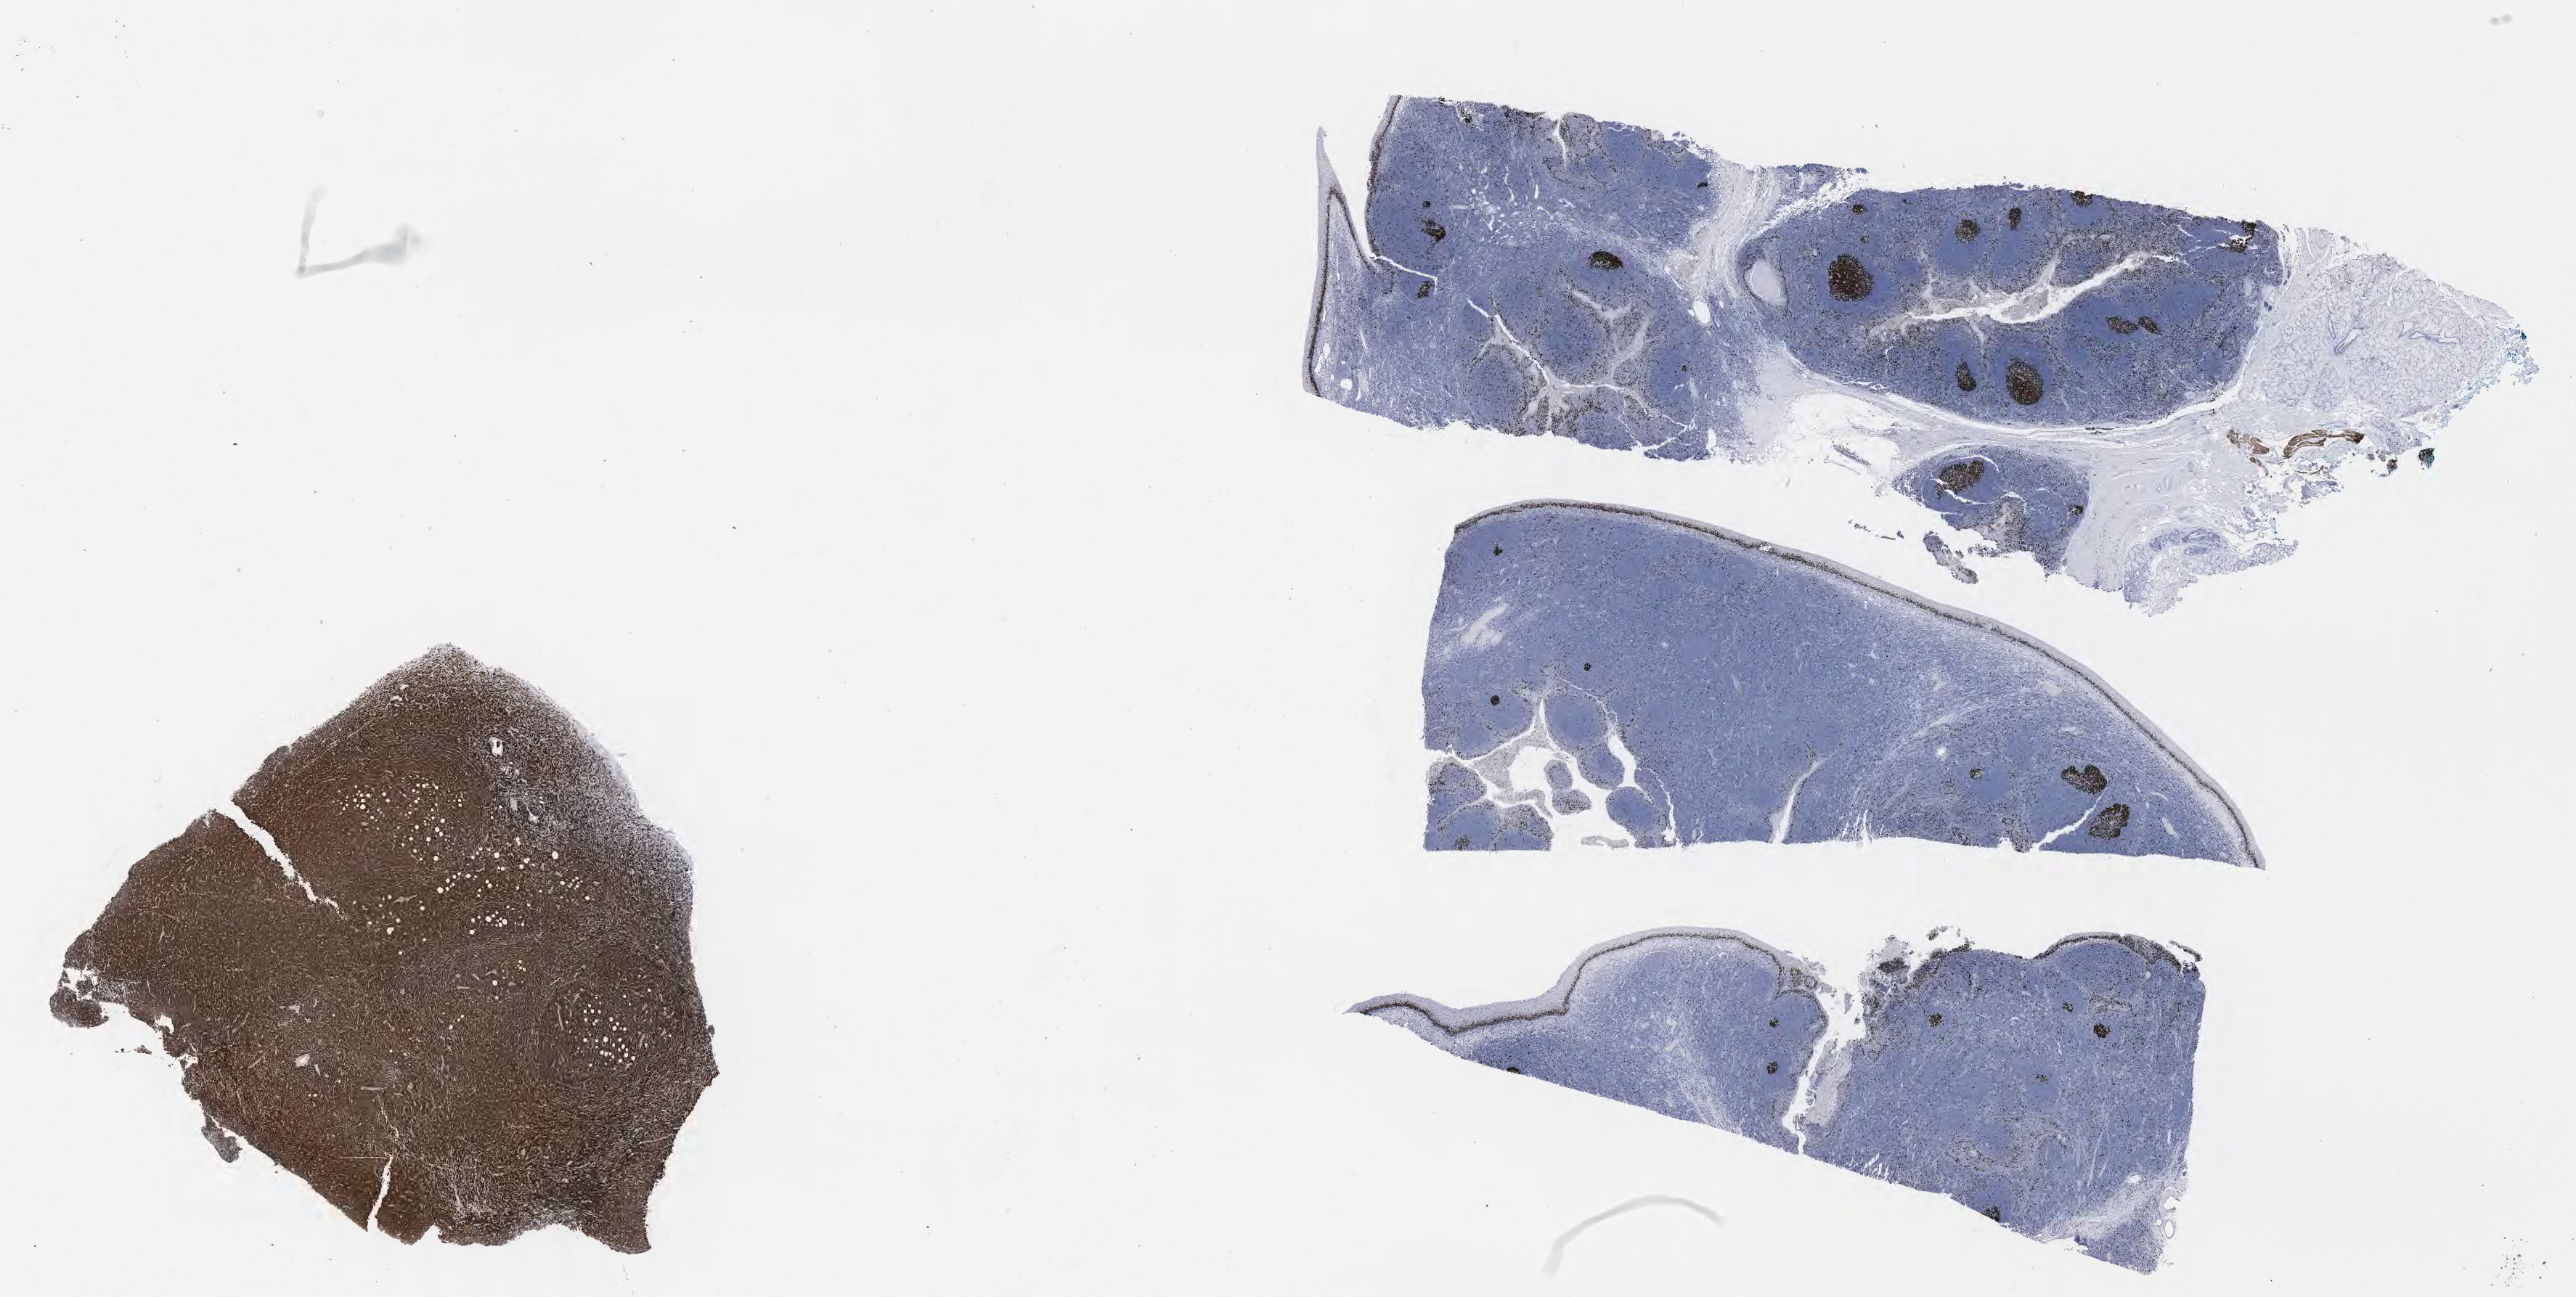
Immunohistochemistry (IHC) whole-slide image stained for Ki-67, whole scanned area (about 28.7 x 14.4 mm) shown as a low-resolution overview, tumor tissue, site: retroperitoneum. Patient: male, age at initial diagnosis 7 years.
* diagnosis: Diffuse large B-cell lymphoma, NOS